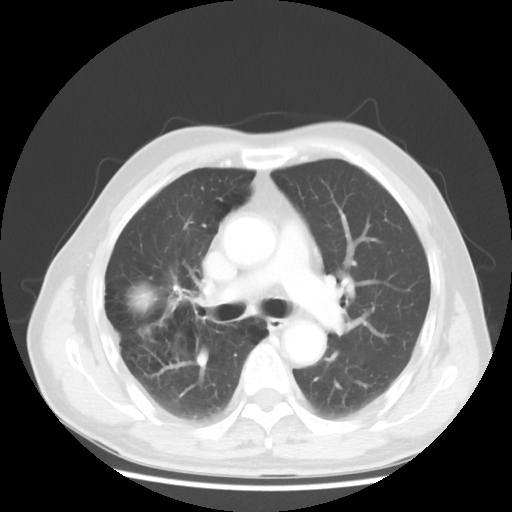
Chest CT, one axial slice; slice 30 of 50 in the series (ordered by position); 120 kVp; lung window (W 1500 / L -600 HU); 5 mm slice thickness; 512 × 512 image matrix, field of view 360 × 360 mm. Male patient, age 69 years. Case-level facts recorded for this patient, not image findings: clinical TNM (as recorded): T3 N0 M0; histopathological grade: G3.
Annotated regions visible in this slice (bounding box drawn by a radiologist):
- lung tumour (recorded histology: adenocarcinoma): bounding box (x1, y1, x2, y2) in pixels: (125, 281, 161, 318)